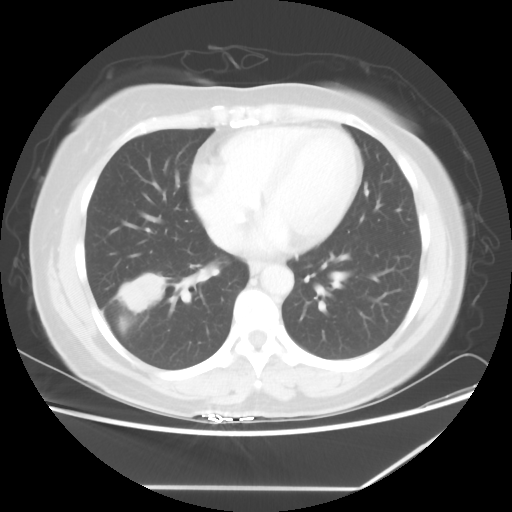
Chest CT, one axial slice; position 25 of 60 along the scan axis; reconstruction kernel STANDARD; 100 kVp; lung window (W 1500 / L -600 HU); 512 × 512 image matrix, field of view 374 × 374 mm. Female patient, age 42 years. Case-level facts recorded for this patient, not image findings: clinical TNM (as recorded): T2 N1 M0.
Structures marked on this image (rectangle marked by the reading radiologist):
- lung tumour (recorded histology: adenocarcinoma): bounding box [x1, y1, x2, y2] px = [113, 268, 166, 316]